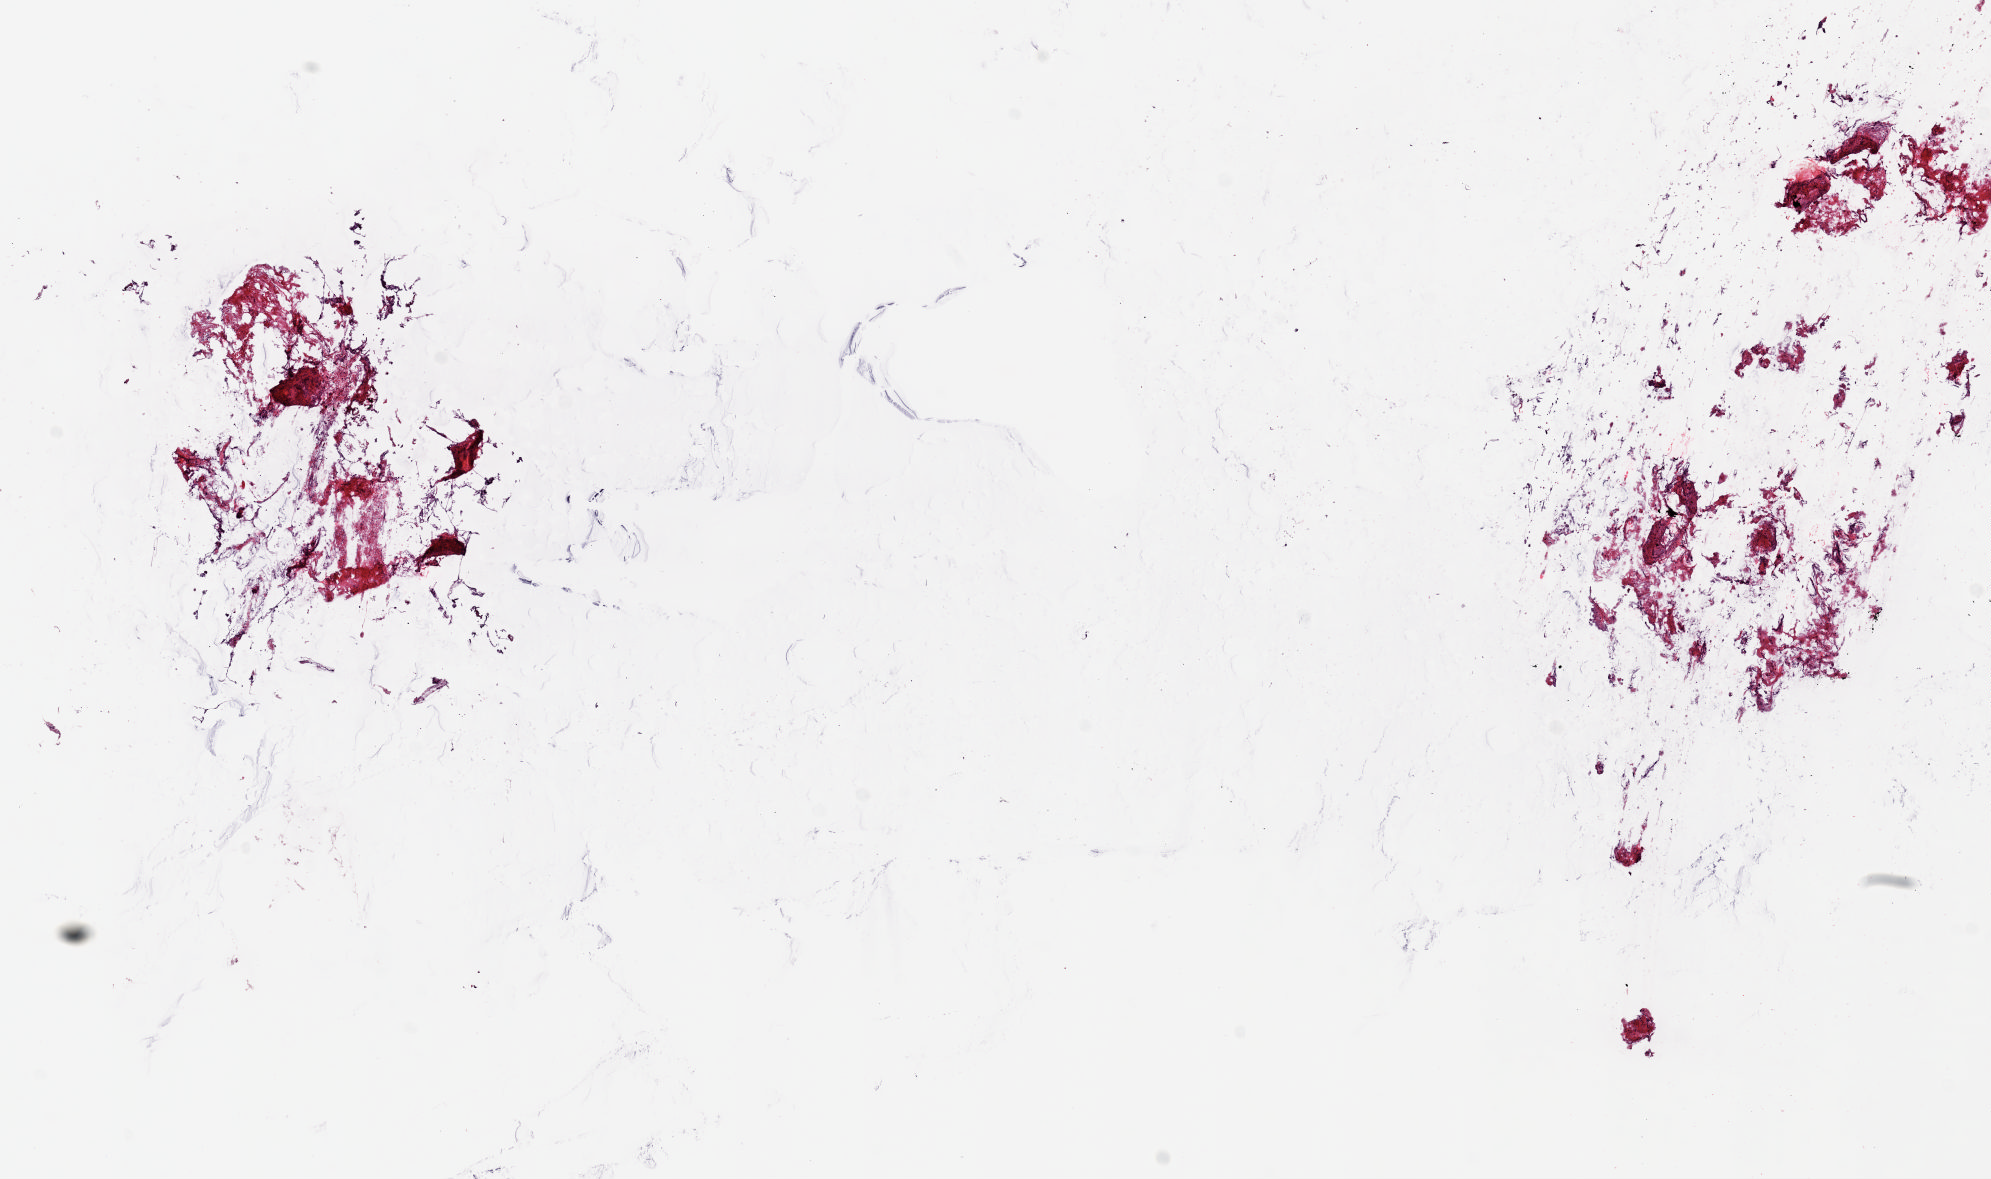
Digitized H&E tissue section (whole slide), a low-resolution overview of the entire scanned area, about 15.7 x 9.3 mm, frozen section from the top of the tissue portion, breast, solid tissue normal (non-tumour tissue) sample. Female, age 62 years at initial diagnosis. Slide review estimates, as recorded: tumour cells 0%, tumour nuclei 0%, normal cells 0%, stromal cells 100%, necrosis 0%. Infiltration values recorded for this section: lymphocyte infiltration 0%, monocyte infiltration 0%, neutrophil infiltration 0%.
• this section: solid tissue normal sample (biorepository sample class)
• patient diagnosis: Lobular carcinoma, NOS